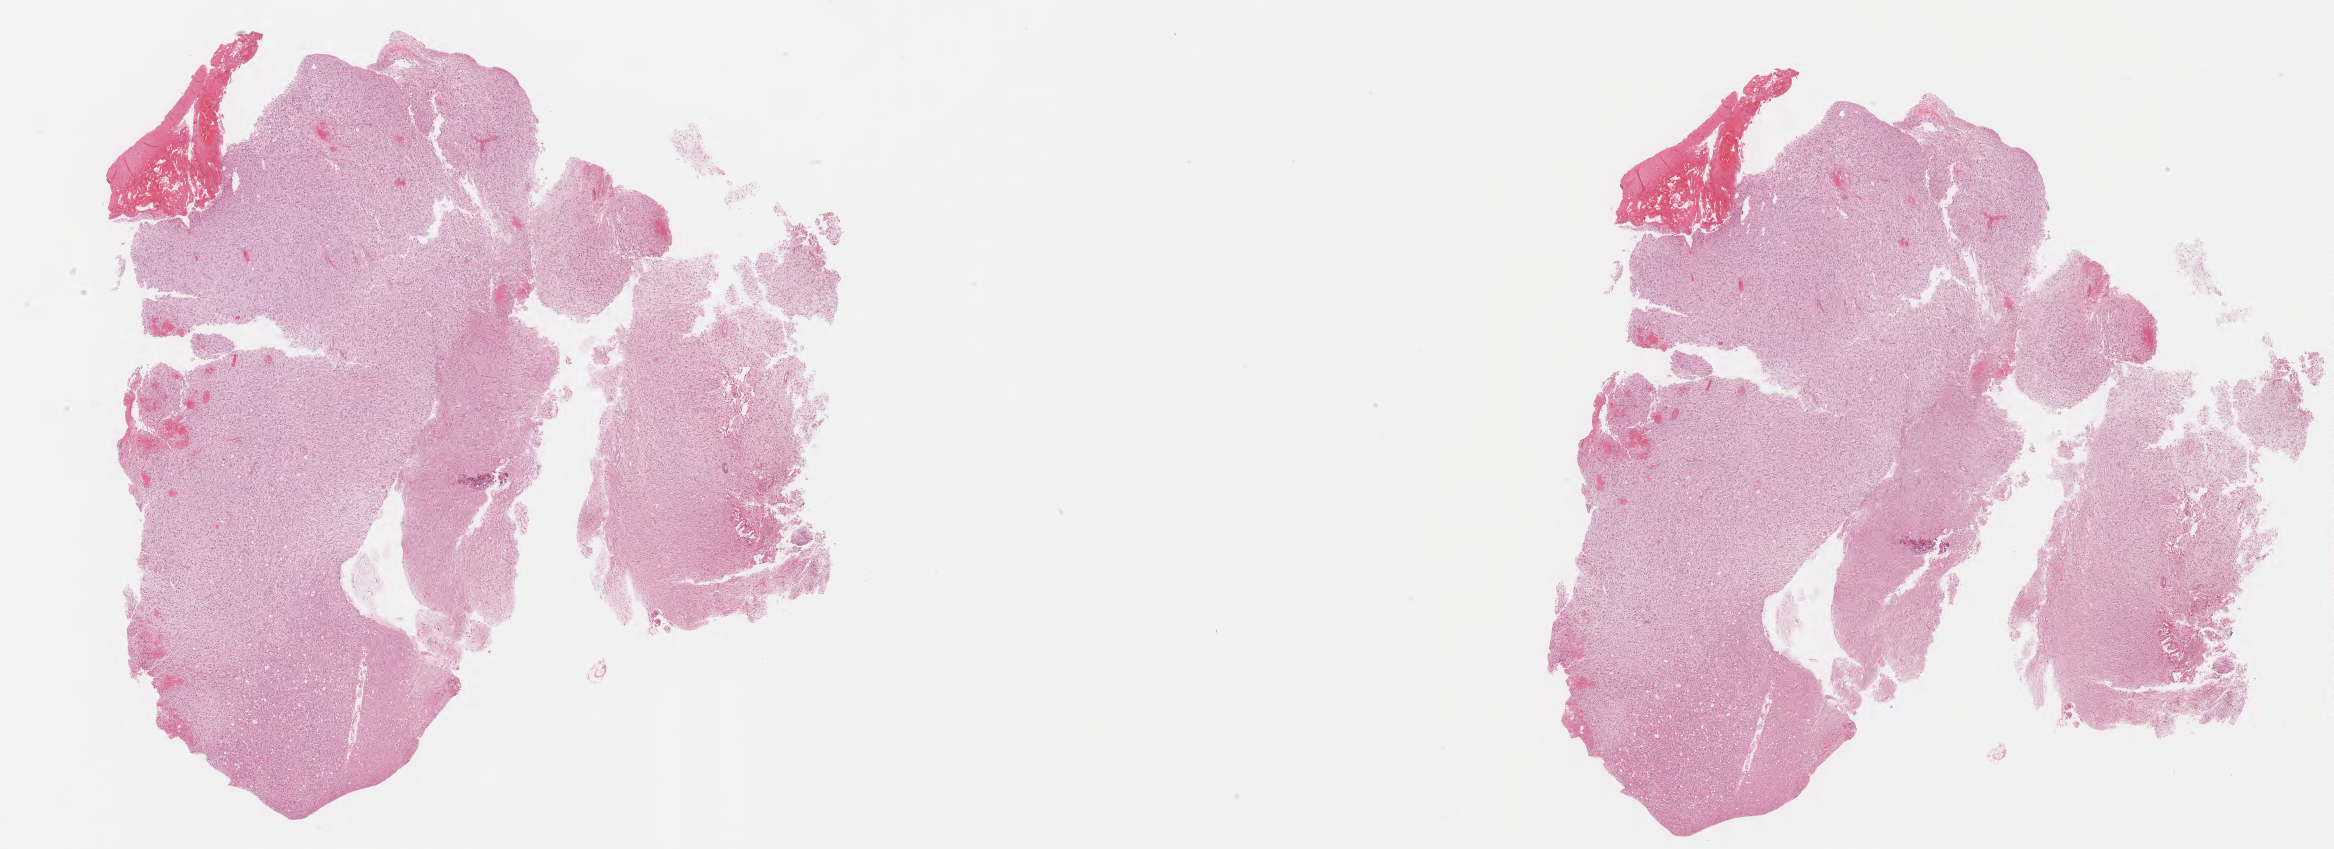
Hematoxylin and eosin (H&E) stained whole-slide image, low-resolution overview of the scanned area, about 36.9 x 13.4 mm (slide scanned at 40x). Formalin-fixed paraffin-embedded (FFPE) diagnostic section. Brain, primary tumour sample. Female, age 36 years at initial diagnosis. Histologic grade: G3 (poorly differentiated).
Histologic diagnosis: Astrocytoma, anaplastic.